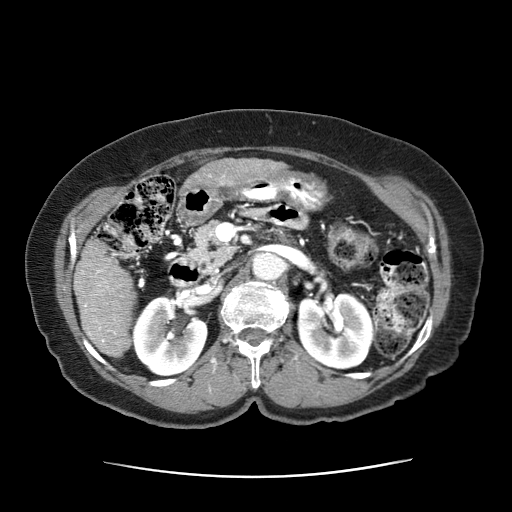
Contrast-enhanced abdominal CT (liver protocol), one axial slice. Slice 17 of 63 in the series (ordered by position). 120 kVp. Intravenous contrast given. Soft-tissue window (W 400 / L 40 HU). 512 × 512 image matrix. Patient: female, 79 years. Case-level facts recorded for this patient, not image findings: diagnosis: hepatocellular carcinoma (patient treated with transarterial chemoembolisation; whether this scan precedes or follows treatment is not stated here); TNM stage (as recorded): Stage-II.
Annotated regions visible in this slice (semi-automatic segmentation, software-assisted and operator-edited):
- abdominal aorta: bounding box [x1, y1, x2, y2] px = [253, 250, 285, 279]
- liver parenchyma outside the tumour (the mass and vessels are separate outlines, so this box may not span the whole liver): [73, 241, 139, 359]
- mass: [182, 160, 289, 190]
- liver vessels: [84, 269, 123, 343]